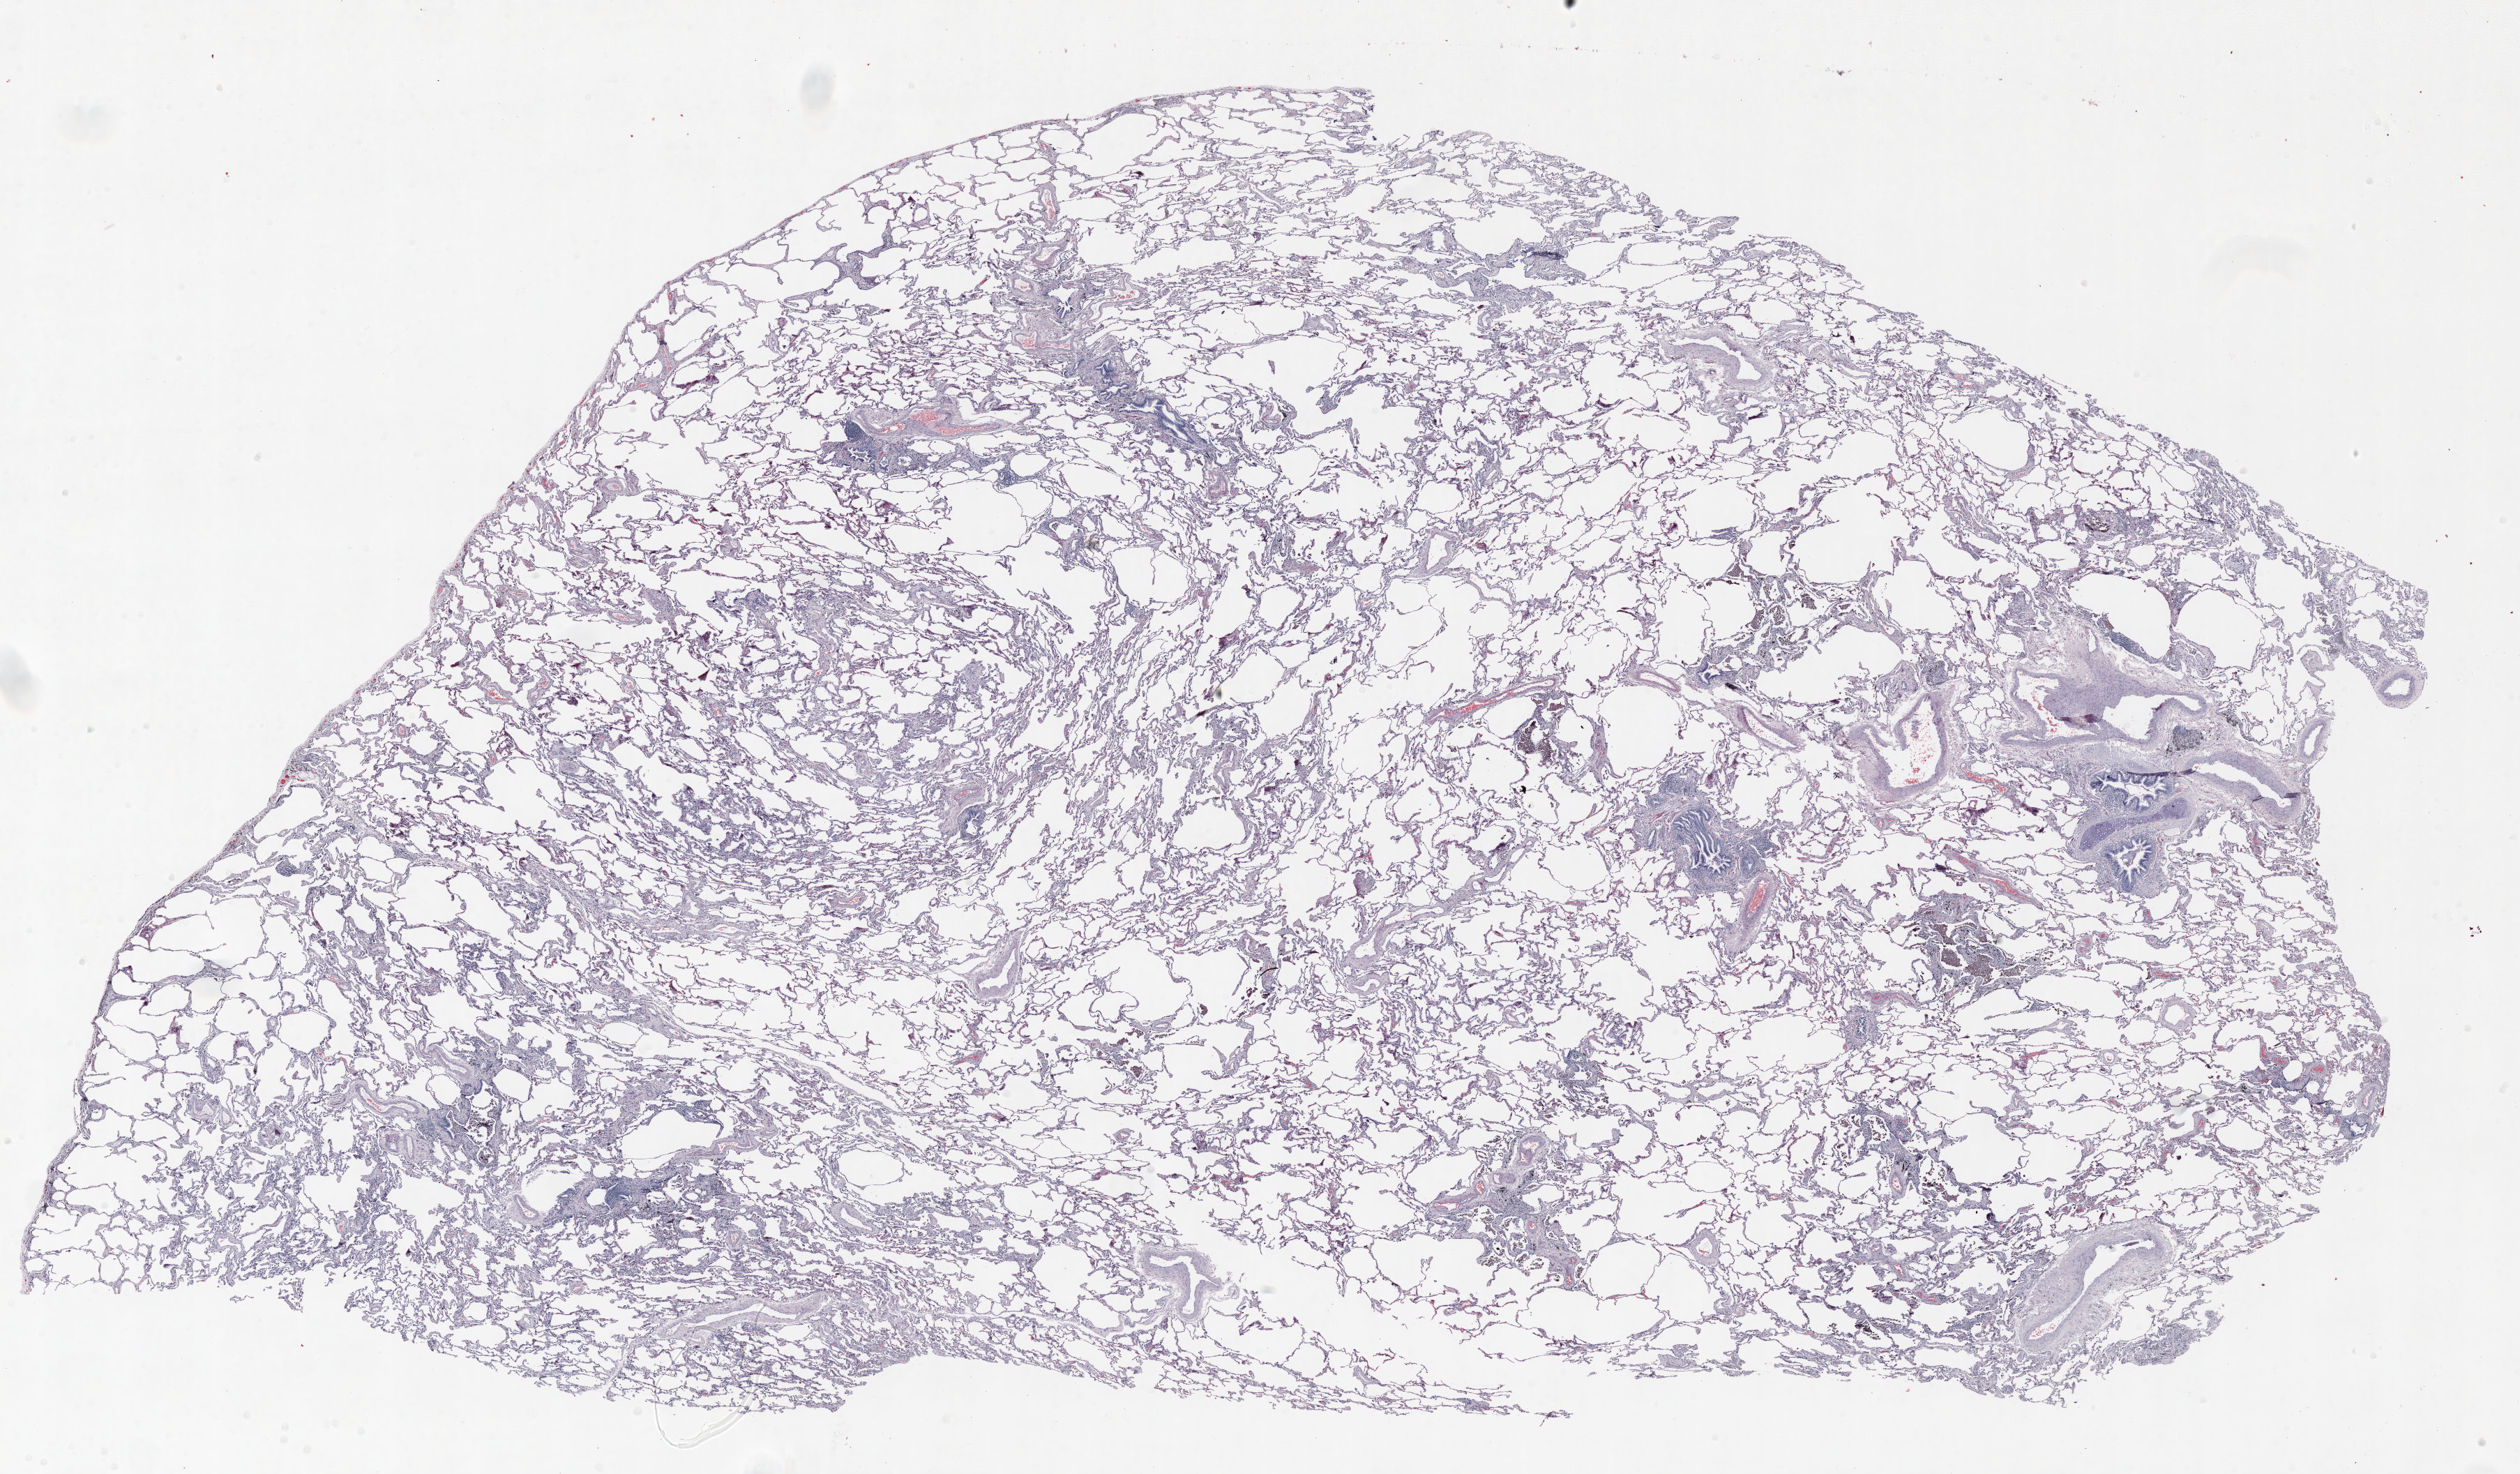
H&E whole-slide image, a low-resolution overview of the entire scanned area, about 29.0 x 17.0 mm. FFPE section. Lung tissue. Female, age 57 at enrolment. Grade: moderately differentiated (G2).
Tumour size (pathology): 30 mm. Primary tumour location (clinical record): right lower lobe. Participant's lung-cancer diagnosis: Adenocarcinoma, NOS. Stage (AJCC 6th edition): IB.